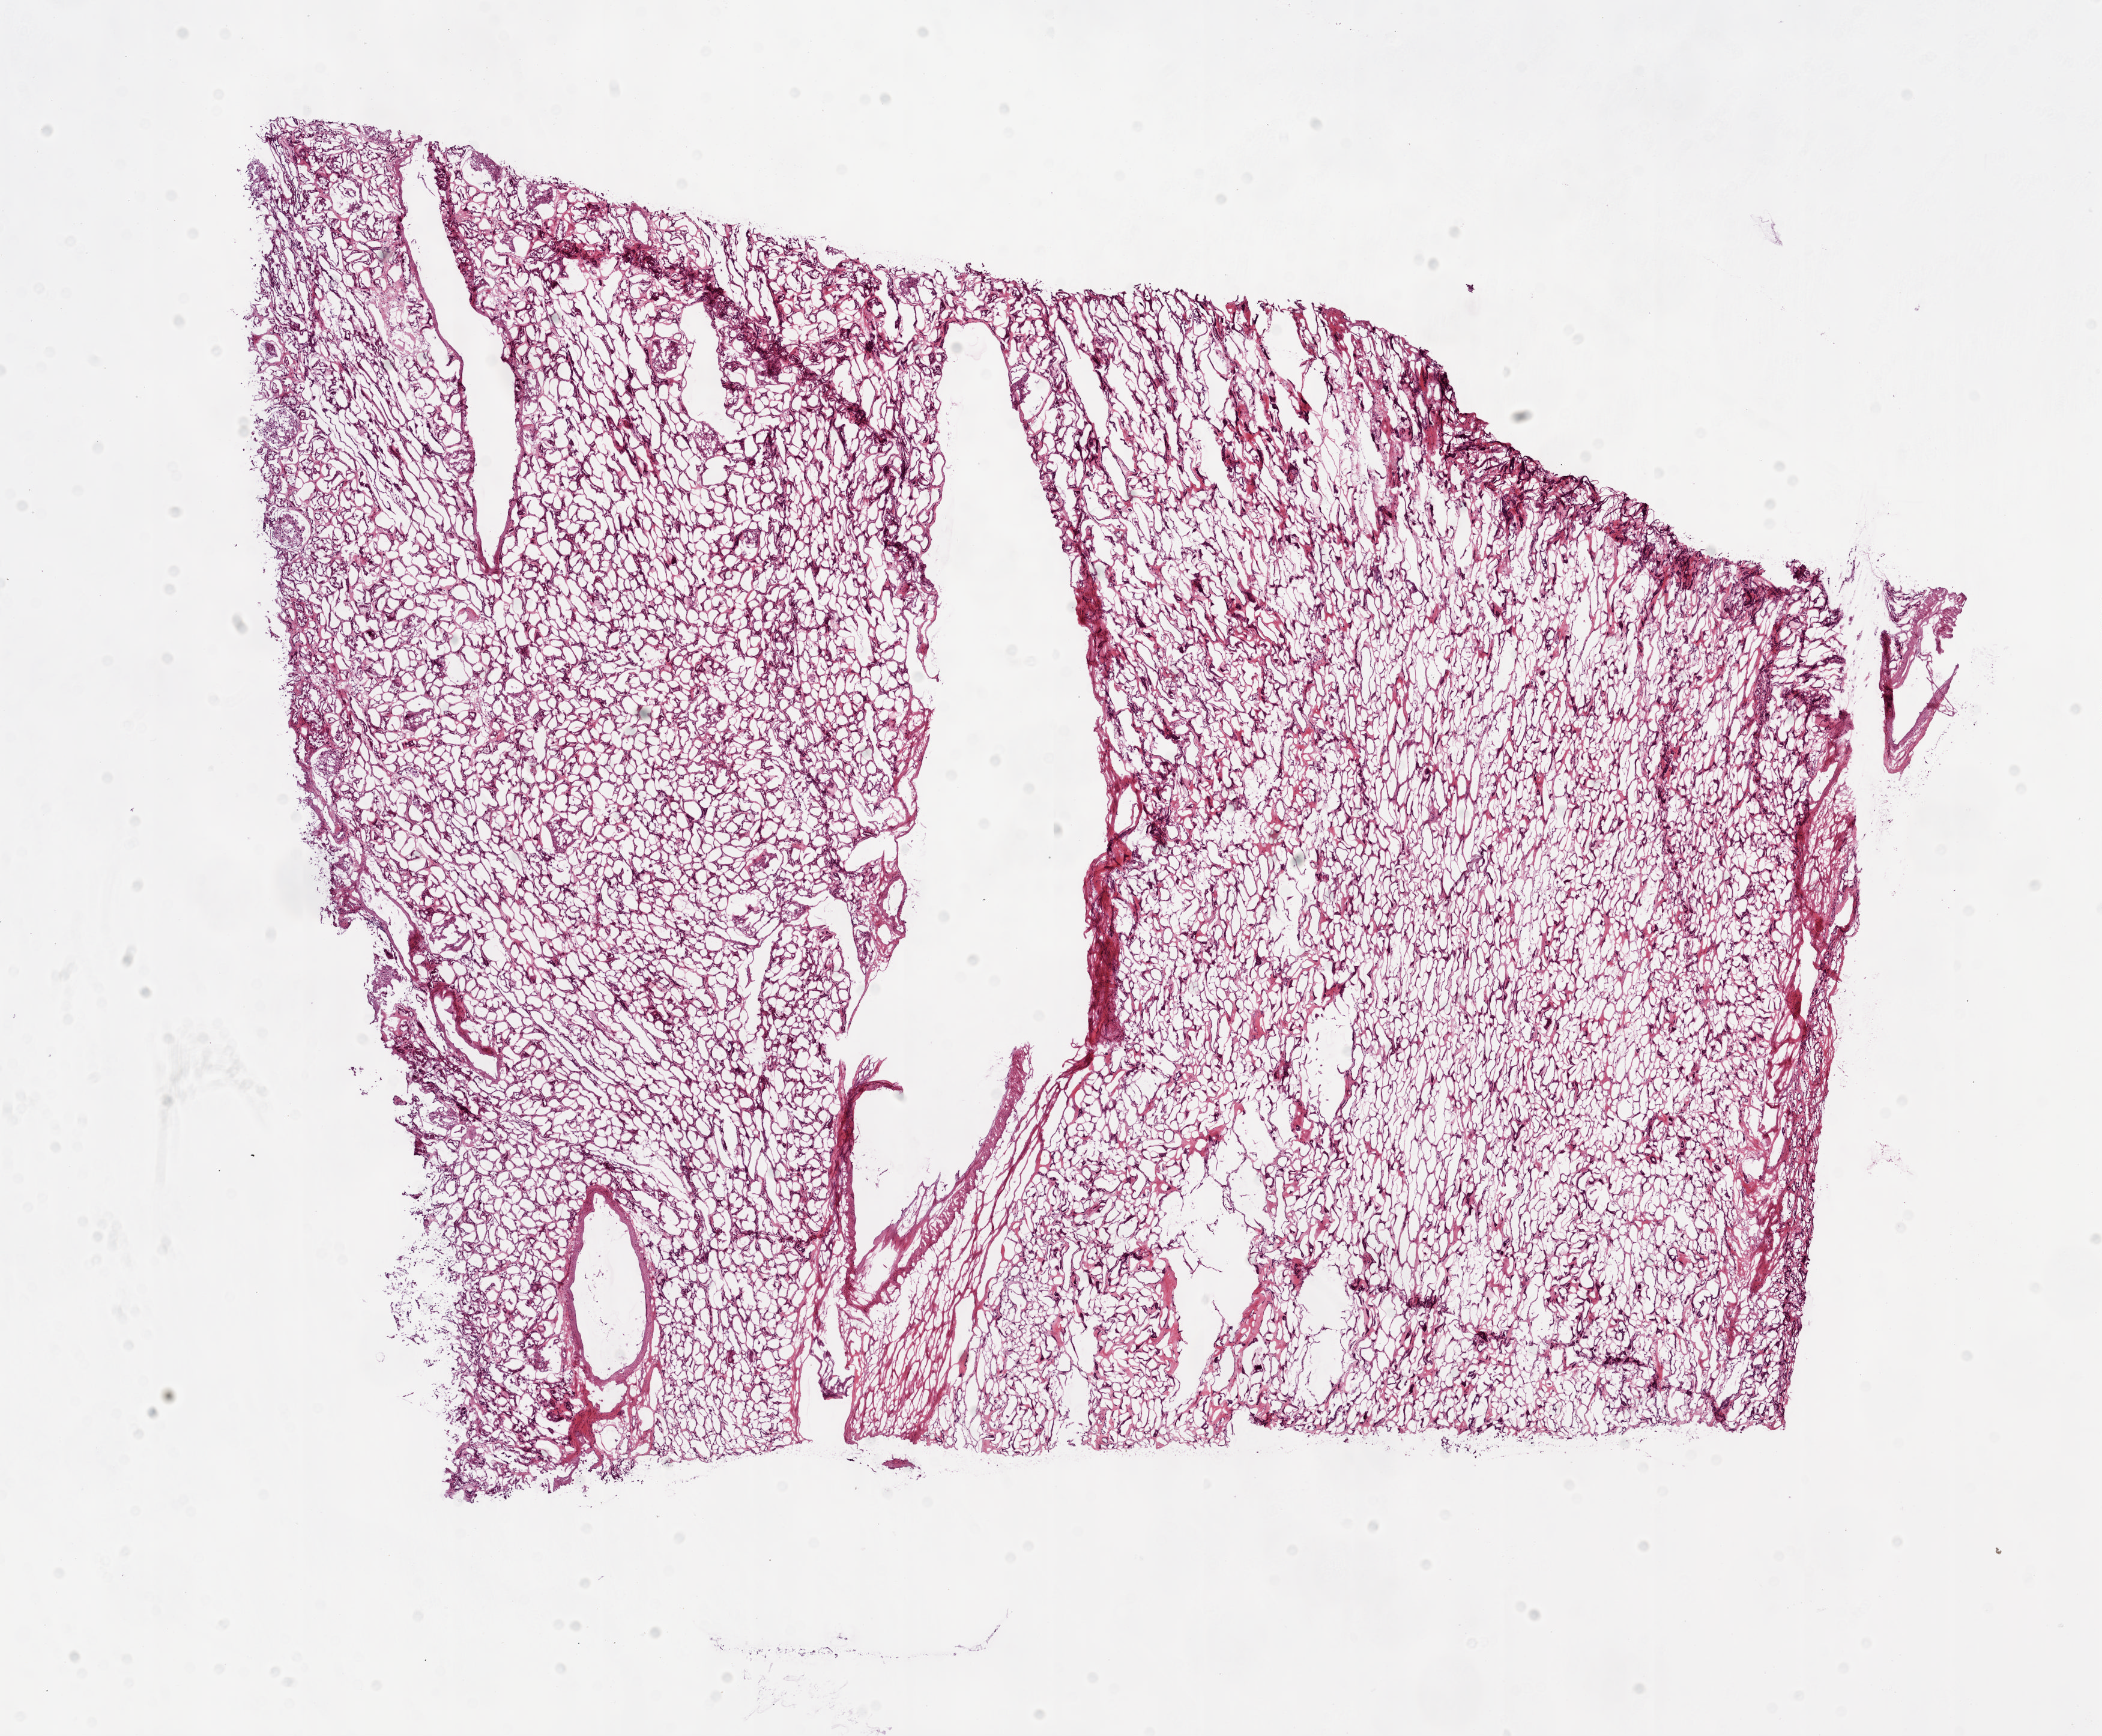
Hematoxylin and eosin (H&E) stained whole-slide image, a low-resolution overview of the entire scanned area, about 13.9 x 11.5 mm. Frozen section from the bottom of the tissue portion. Kidney, solid tissue normal (non-tumour tissue) sample. Patient: male, age at initial diagnosis 57 years.
- this section: solid tissue normal (non-tumour) sample from the same patient
- patient diagnosis: Clear cell adenocarcinoma, NOS